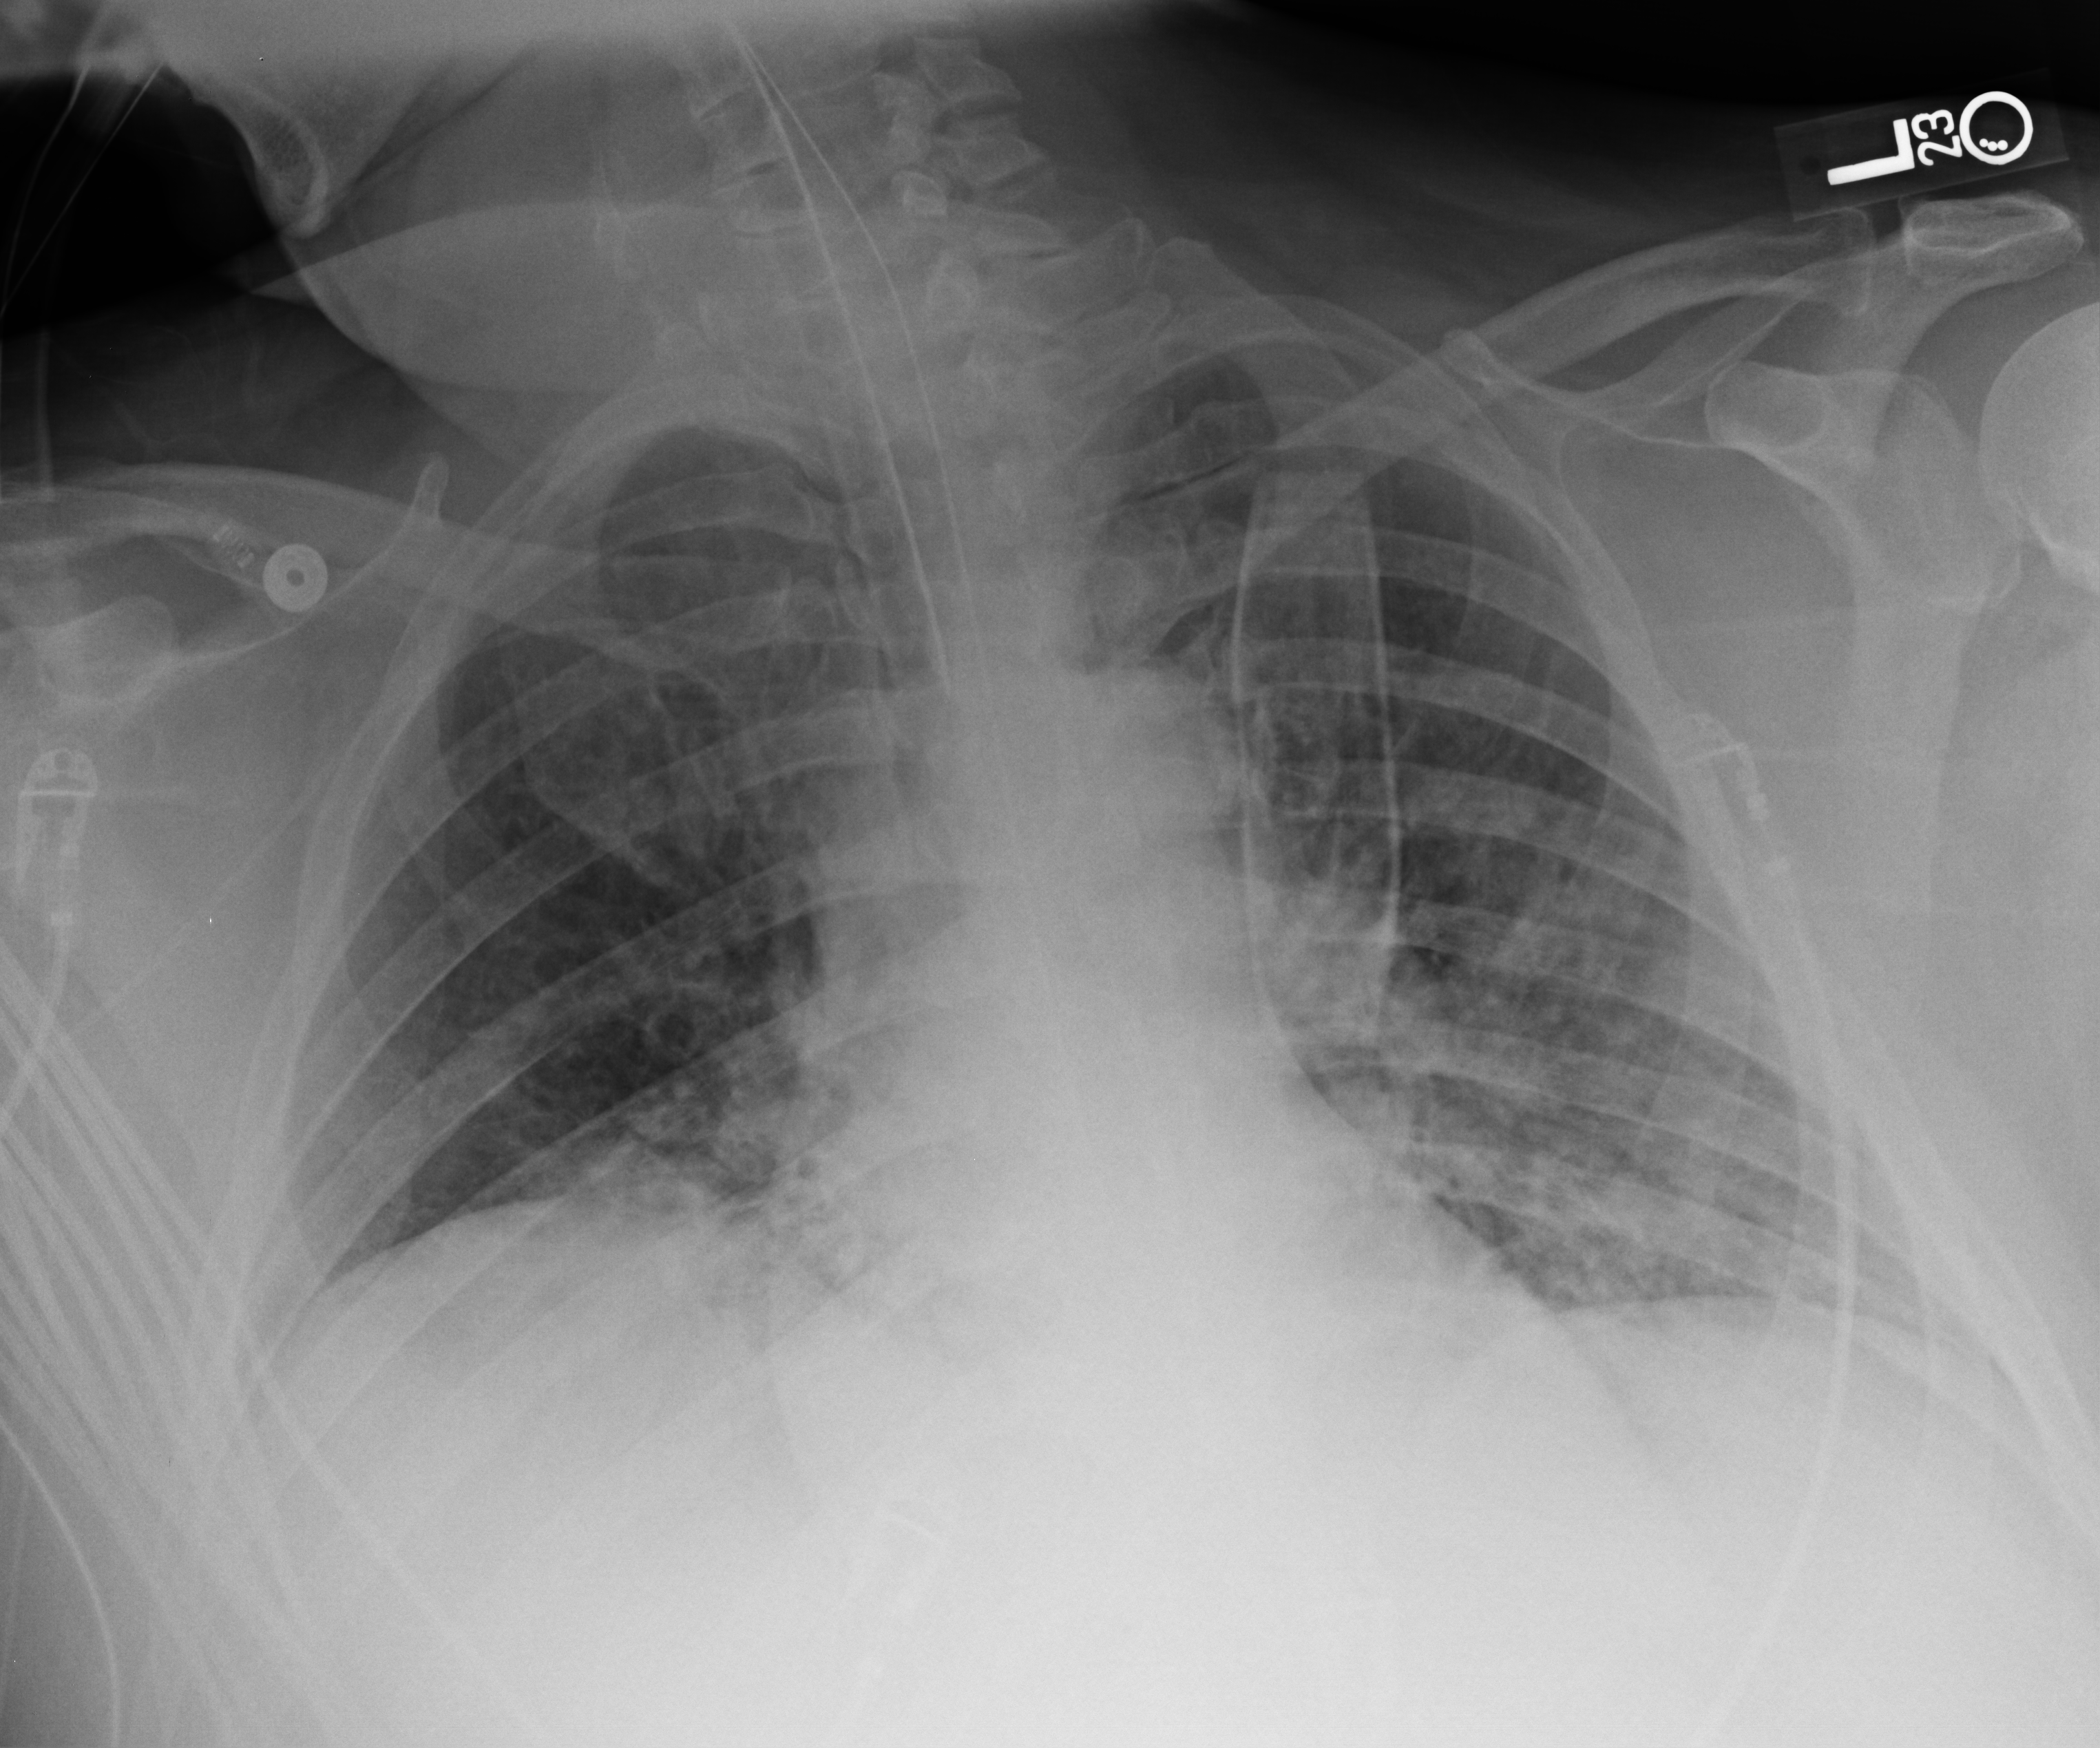
Bedside chest radiograph (computed radiography), anteroposterior (AP) projection. Patient hospitalised with COVID-19; male, aged 18–59 years.
Hospital-stay facts (about this admission, not read from this image; timing relative to this image not recorded): length of hospital stay: 28 days.